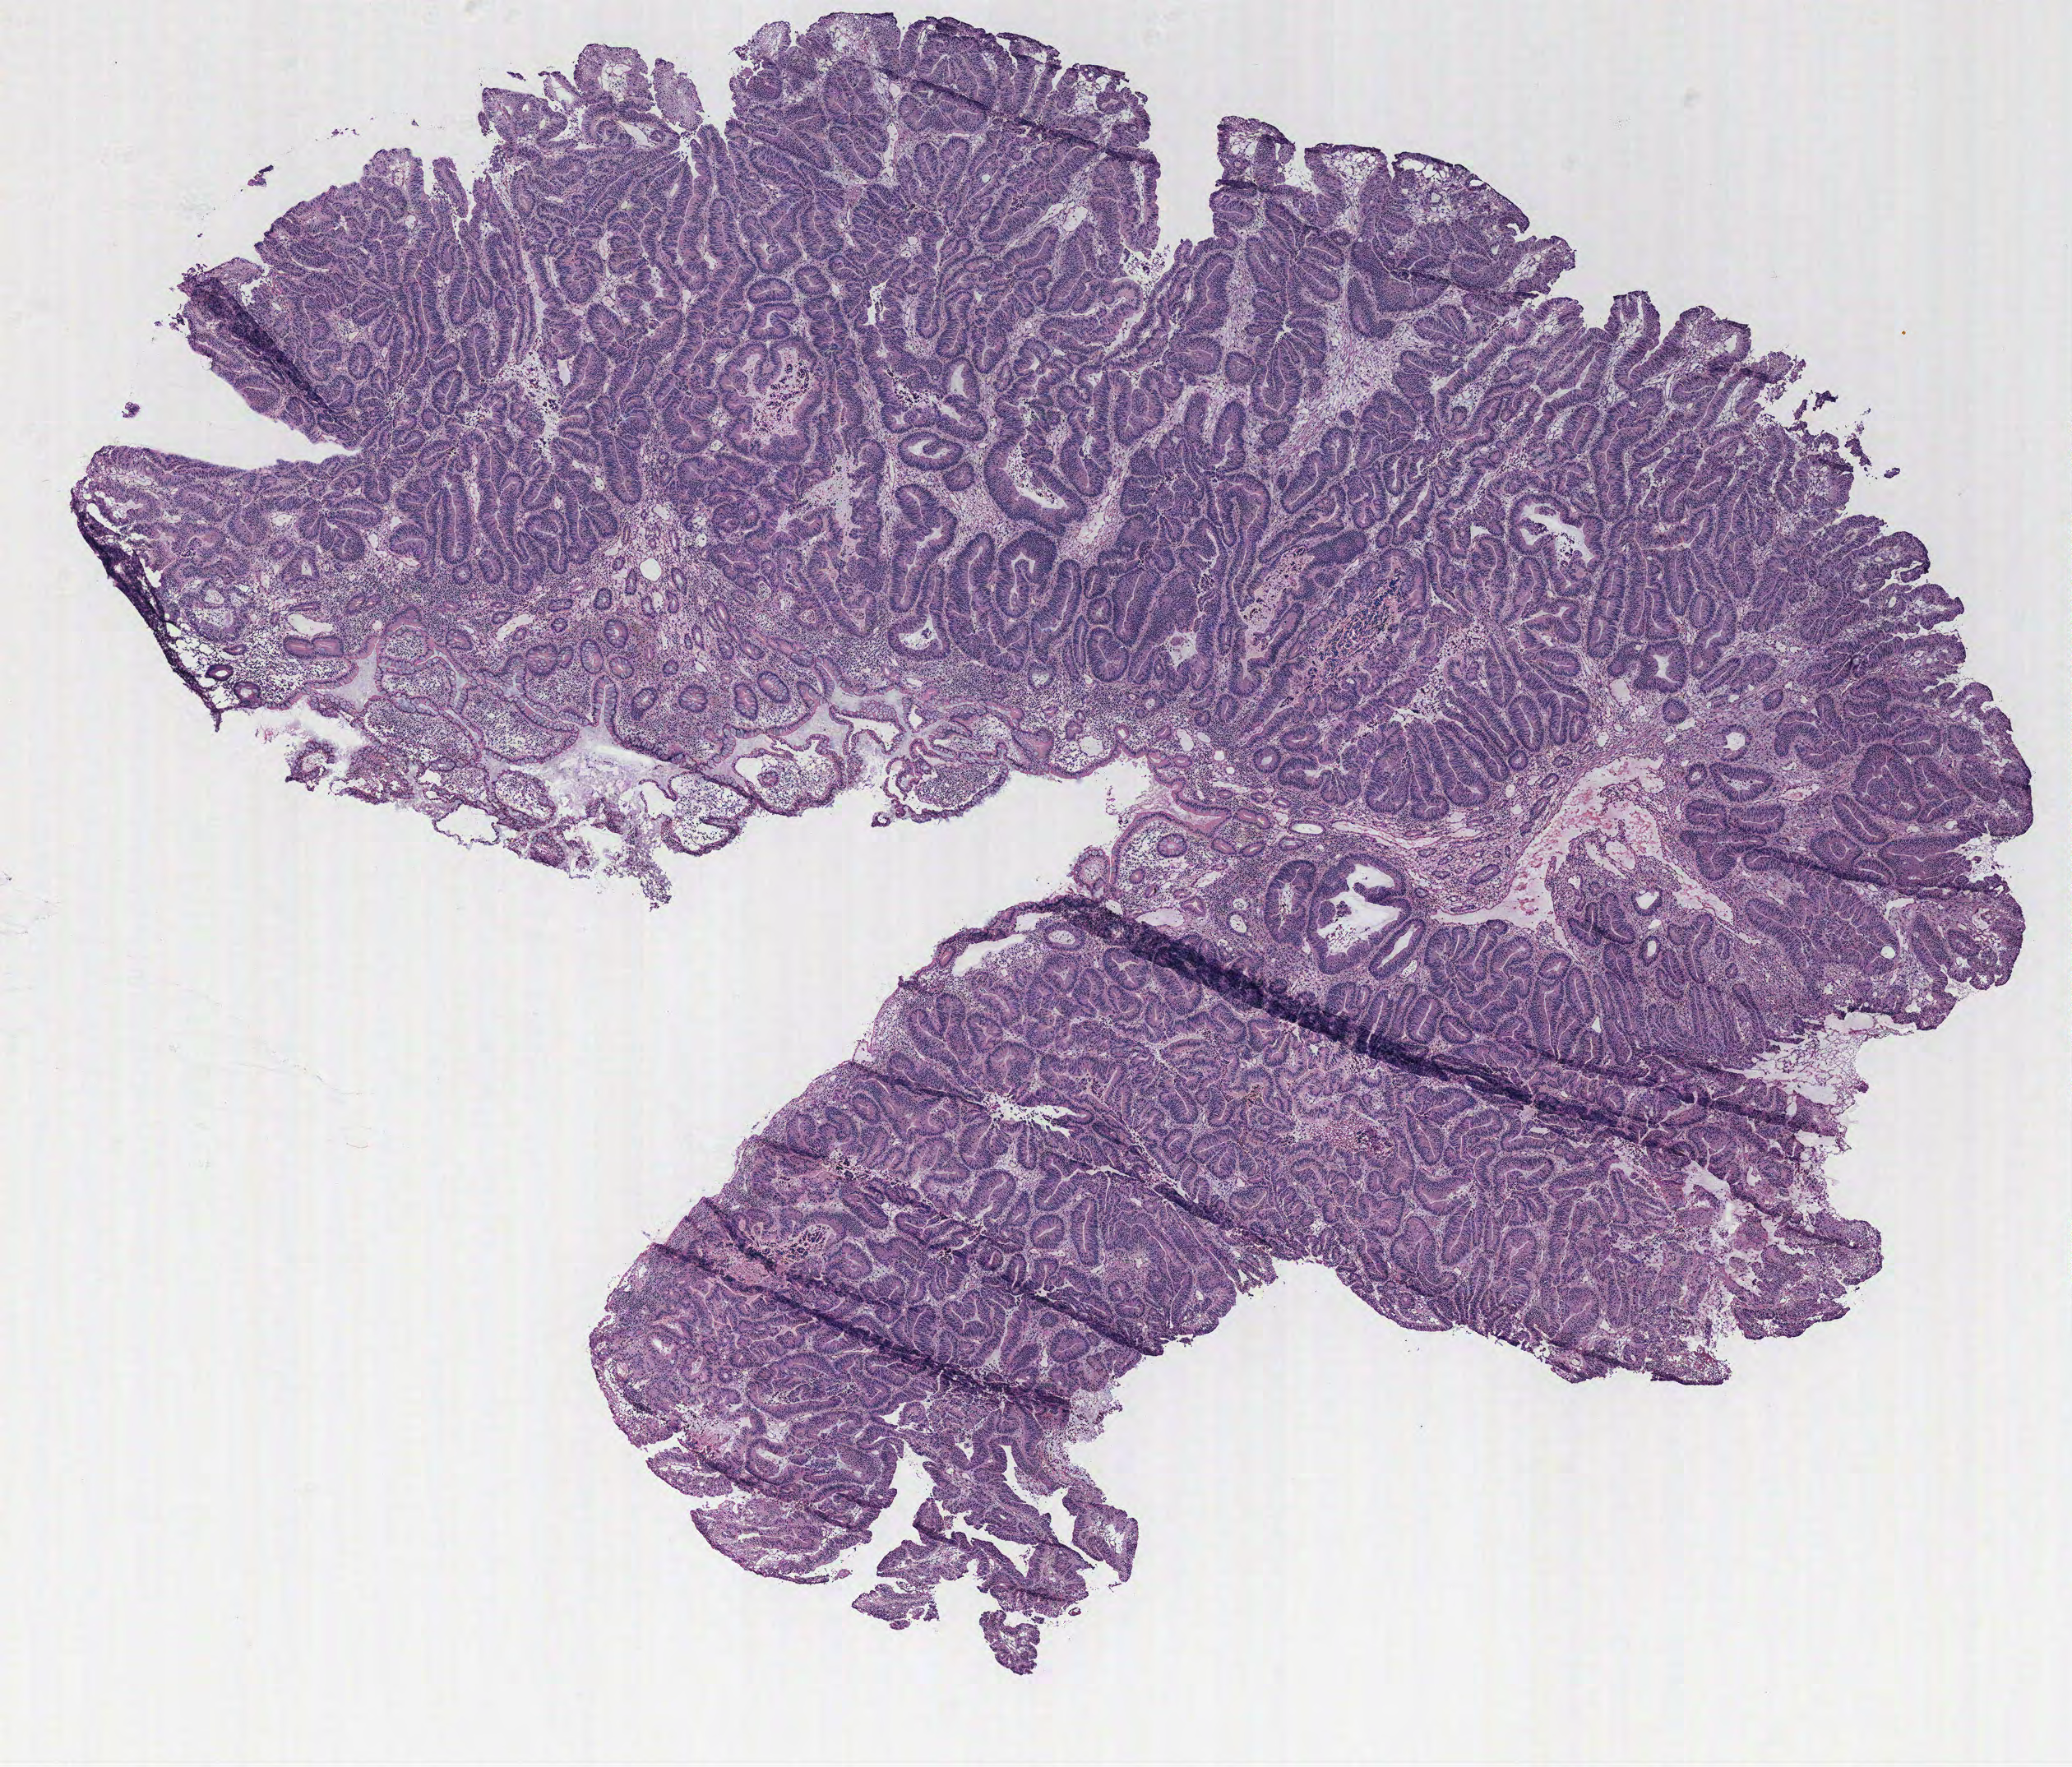
Whole-slide histology image, H&E, a low-resolution overview of the entire scanned area, about 10.1 x 8.6 mm. Colon, normal (non-tumour) tissue. 58-year-old male patient.
This section: normal (non-tumour) tissue from the same patient. Patient diagnosis (cohort enrolment): colon cancer (colon).